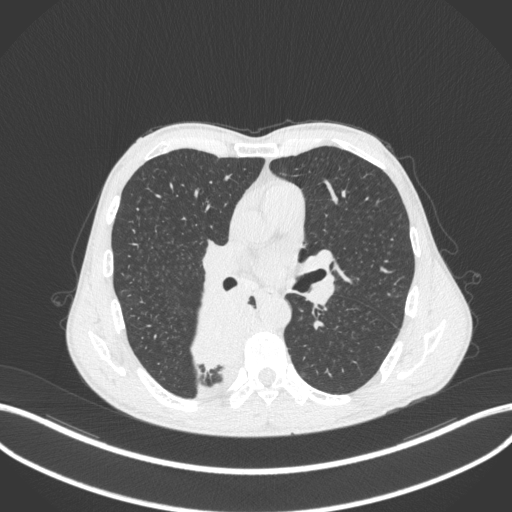
Chest CT, one axial slice. Slice 210 of 371 in the series (ordered by position). 120 kVp. Lung window (W 1500 / L -600 HU). 1 mm slice thickness. 512 × 512 image matrix. Patient: male, 58 years. Case-level facts recorded for this patient, not image findings: clinical TNM (as recorded): T3 N1 M1.
Outlined on this slice (rectangle marked by the reading radiologist):
- lung tumour (recorded histology: squamous cell carcinoma): bounding box (x1, y1, x2, y2) in pixels: (191, 286, 259, 378)